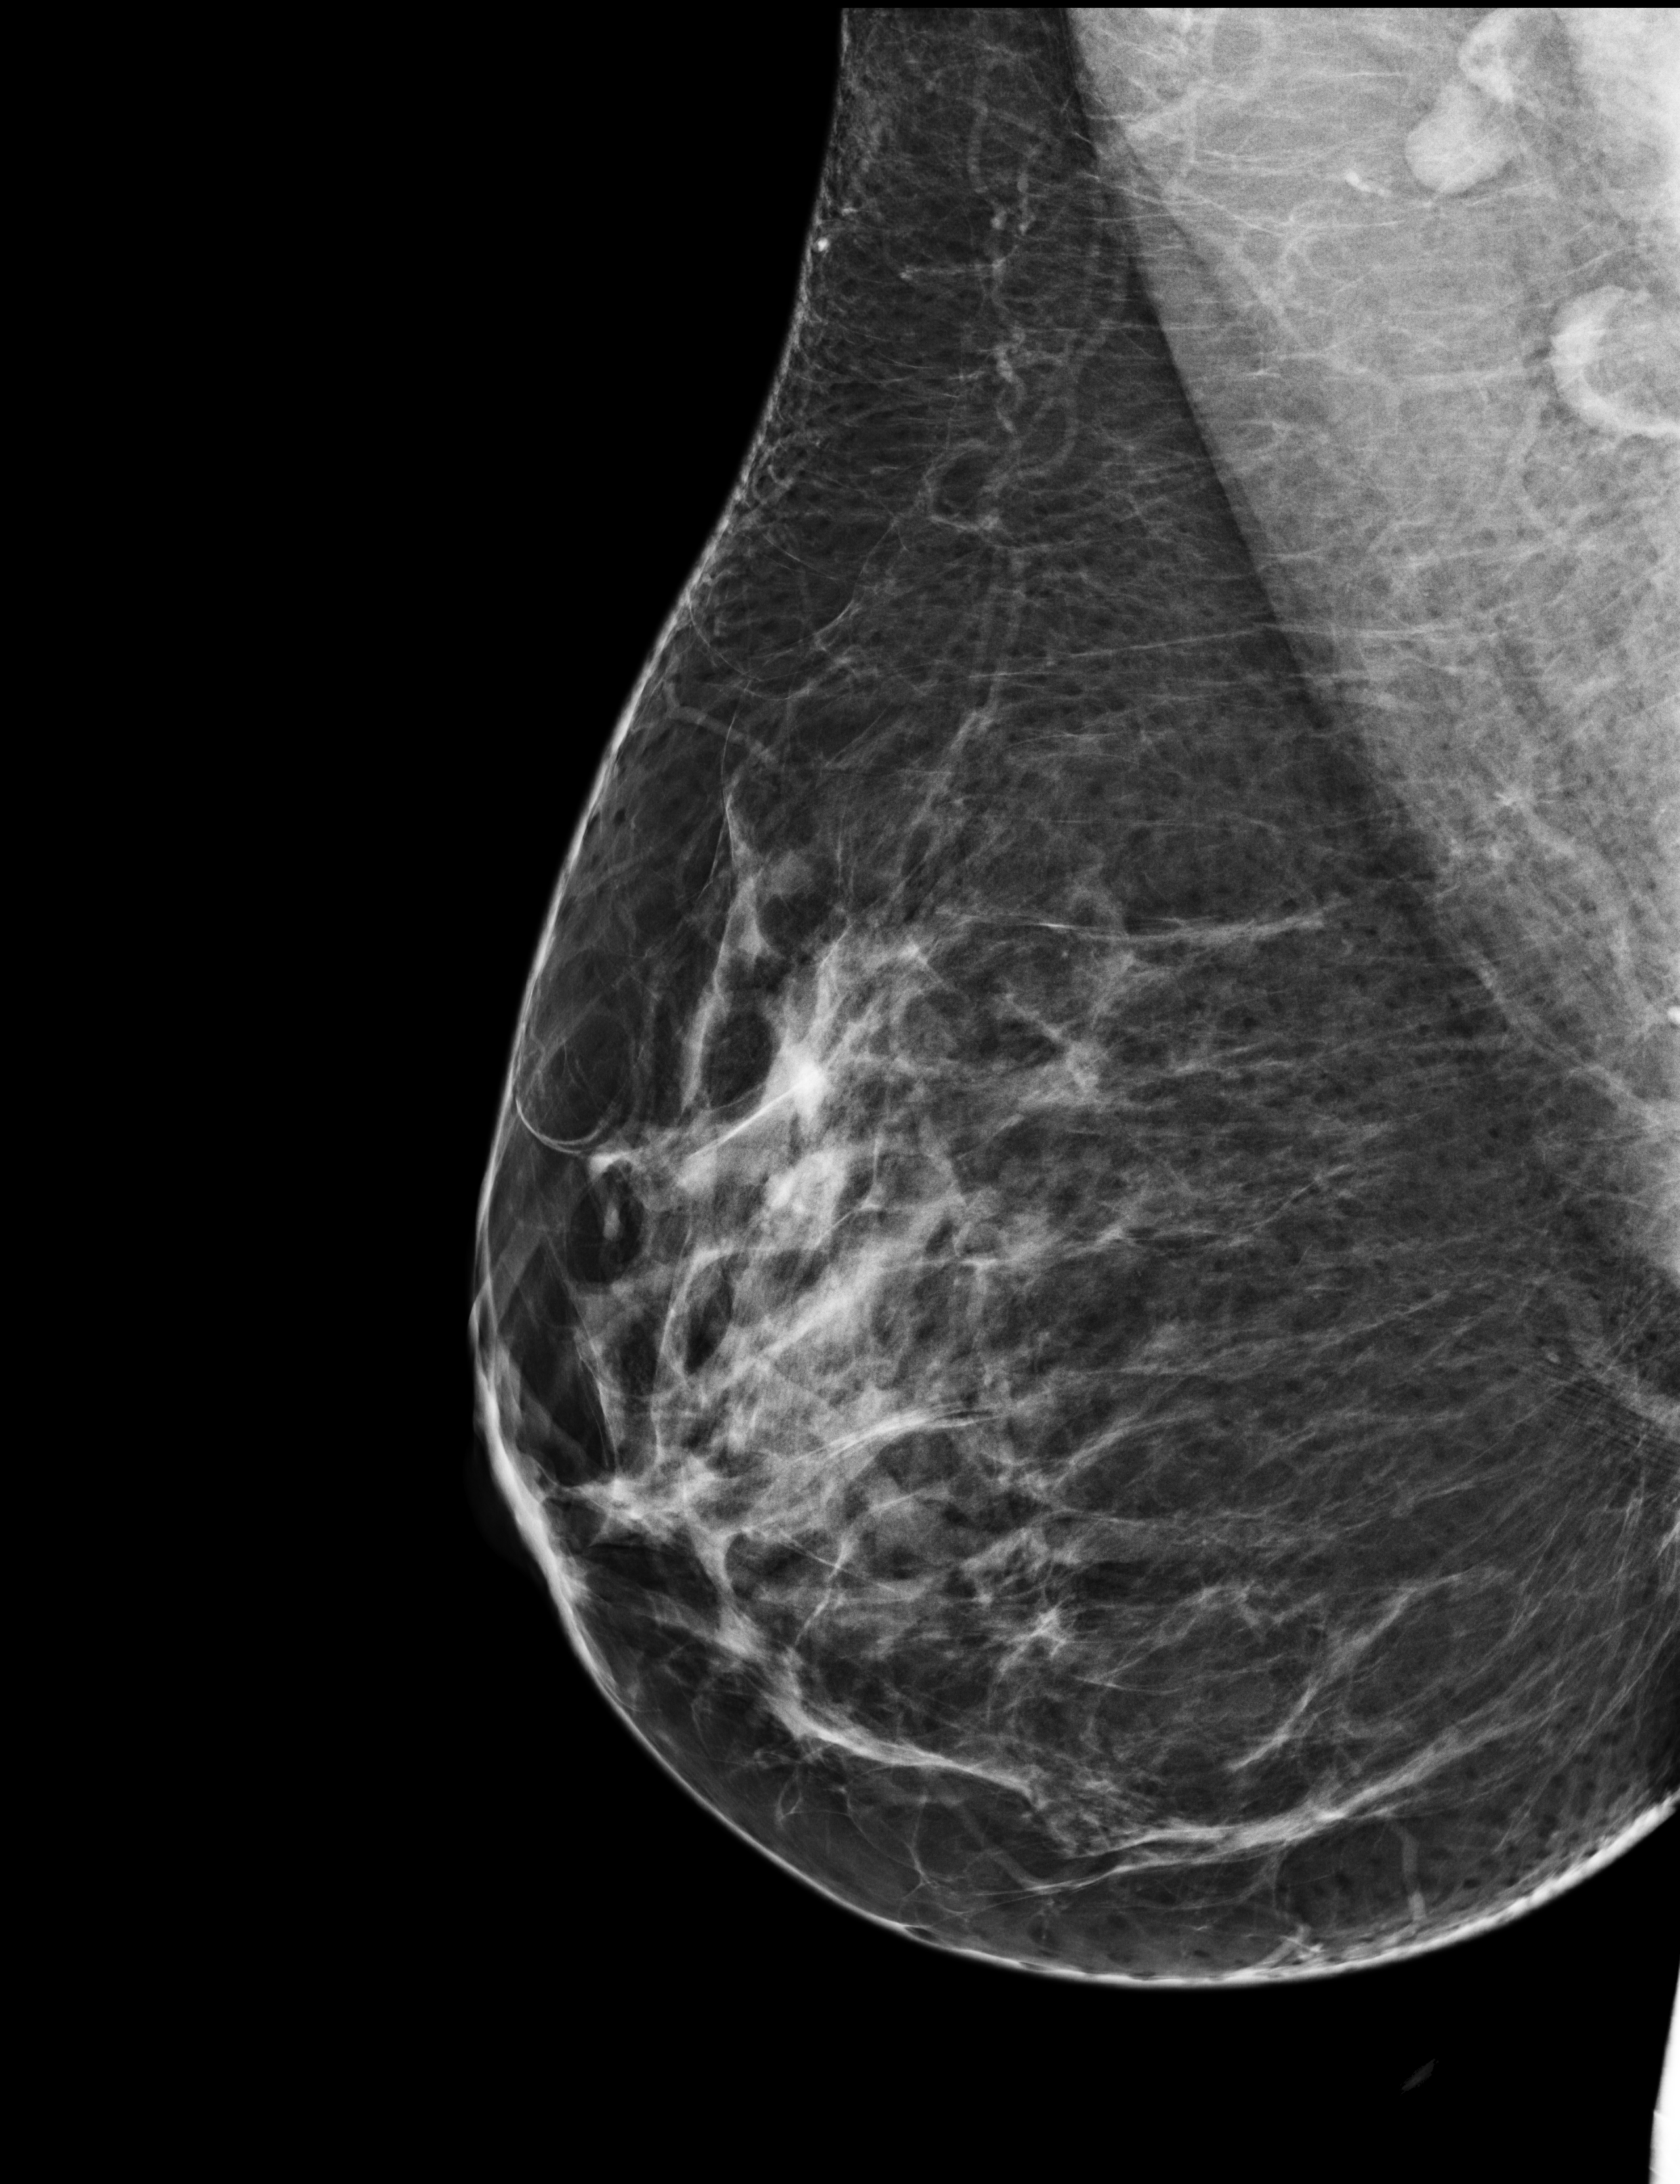
Screening examination; system: Selenia Dimensions. Patient: female, 42 years.
Image type: full-field digital mammogram. Breast: right. Projection: MLO view.